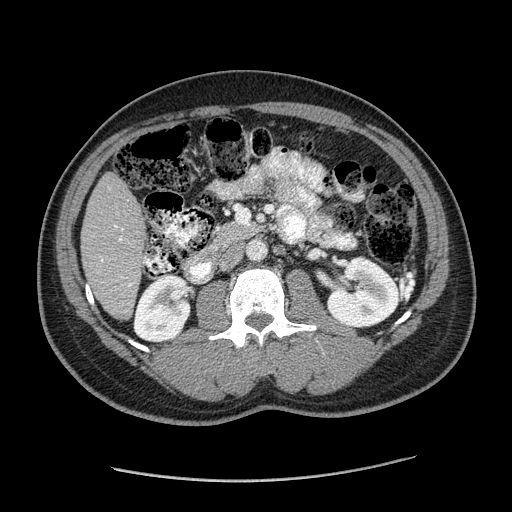
Contrast-enhanced abdominal CT (liver protocol), one axial slice; position 57 of 182 along the scan axis; reconstruction kernel STANDARD; soft-tissue window (W 400 / L 40 HU); 512 × 512 image matrix. From the clinical record (not read from this slice): diagnosis: hepatocellular carcinoma (patient treated with transarterial chemoembolisation; whether this scan precedes or follows treatment is not stated here); TNM stage (as recorded): Stage-I; Child-Pugh class: A; tumour differentiation: well differentiated; tumour nodularity: uninodular.
Annotated regions visible in this slice (semi-automatically segmented with operator editing):
- liver parenchyma outside the tumour (the mass and vessels are separate outlines, so this box may not span the whole liver): bounding box (x1, y1, x2, y2) in pixels: (80, 172, 146, 318)
- liver vessels: (101, 225, 132, 286)